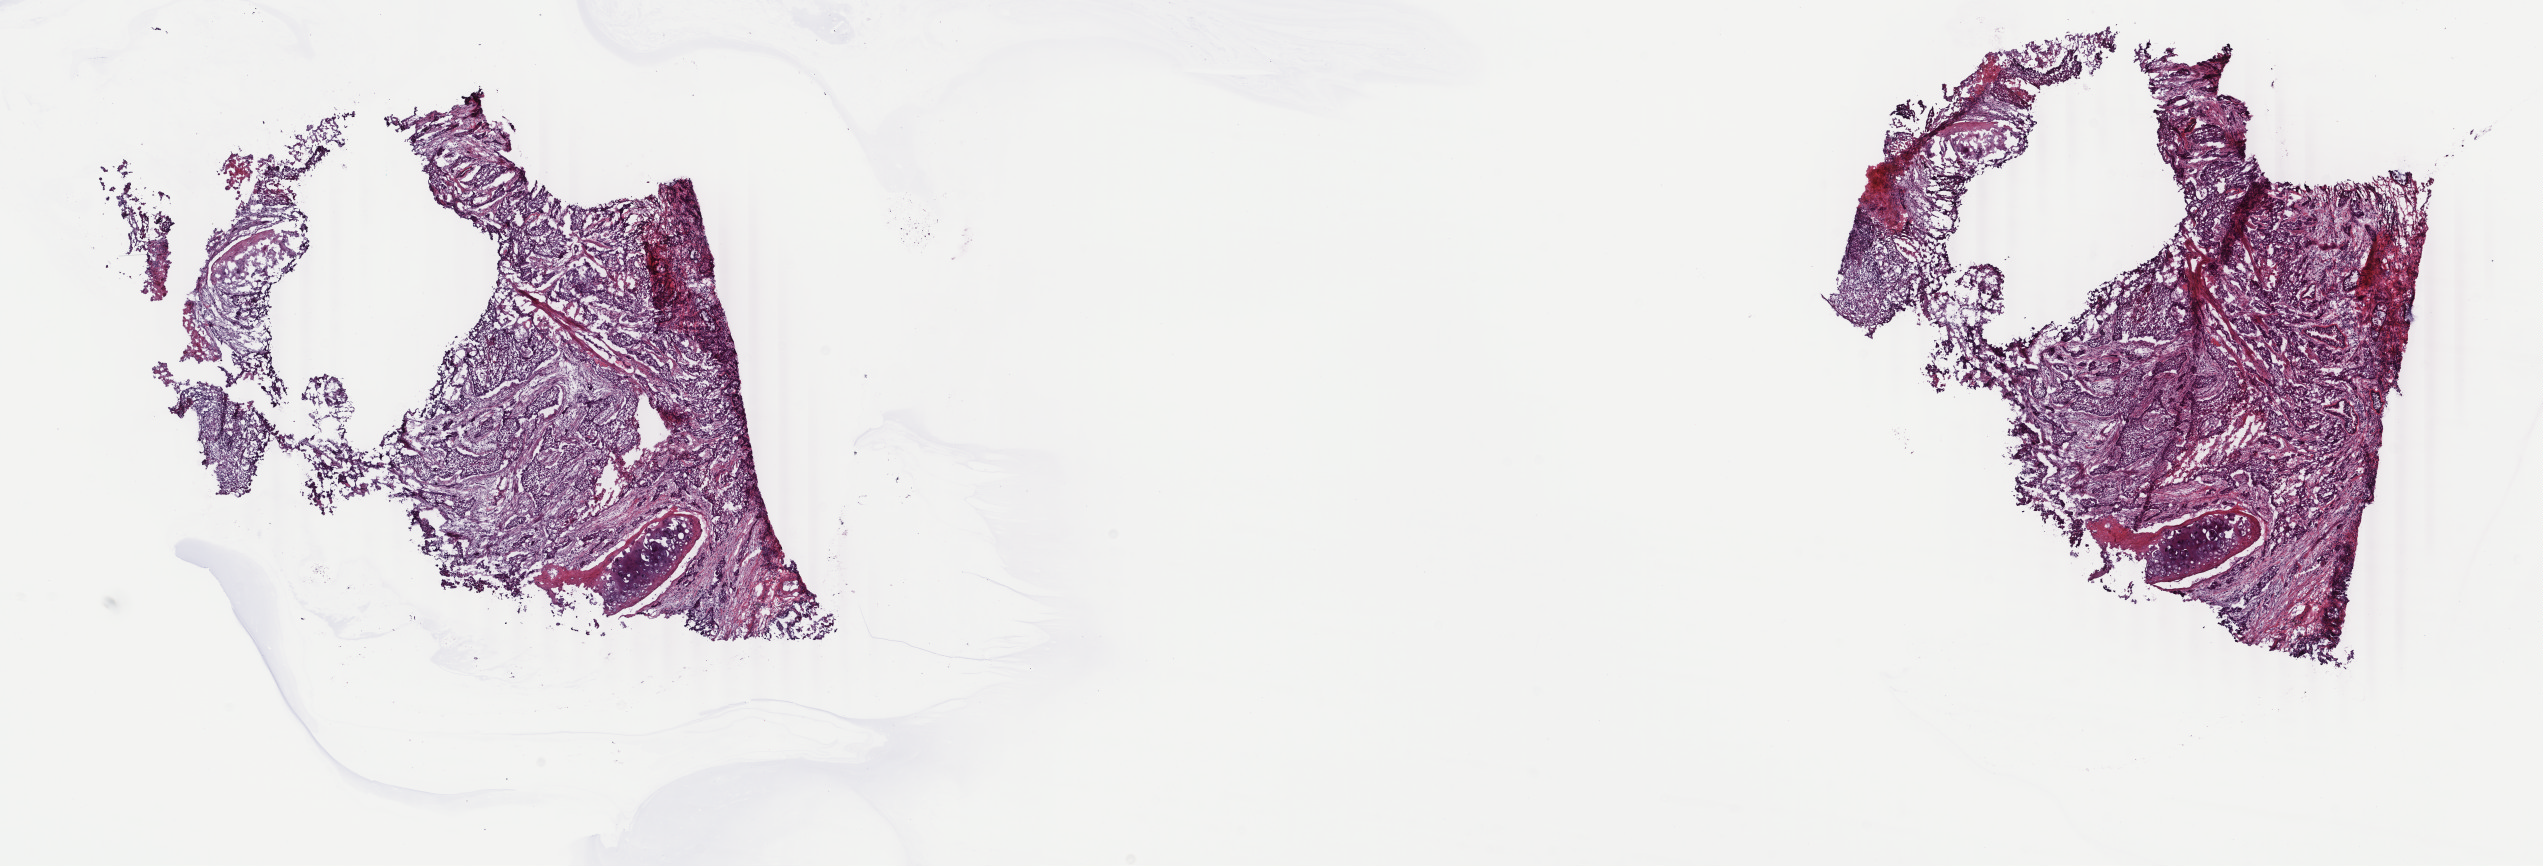
Whole-slide histology image, H&E, whole scanned area (about 20.2 x 6.9 mm) shown as a low-resolution overview; frozen section; primary tumour sample from the lung. Patient: male, age at initial diagnosis 69 years. Slide review estimates, as recorded: tumour cells 95%, tumour nuclei 75%, normal cells 5%, stromal cells 0%, necrosis 0%. Inflammatory infiltration, as recorded: lymphocyte infiltration 0%, monocyte infiltration 0%, neutrophil infiltration 0%.
Histologic diagnosis: Squamous cell carcinoma, keratinizing, NOS (upper lobe, lung). Laterality: left. AJCC pathologic stage: IV (7th edition).